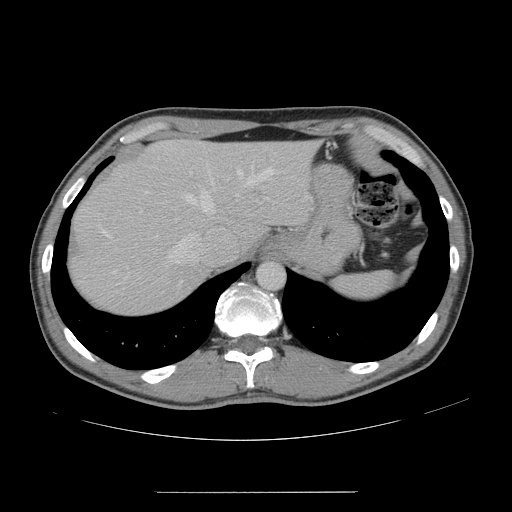
Contrast-enhanced abdominal CT, one axial slice. Position 122 of 178 along the scan axis. 120 kVp. Intravenous contrast given. Soft-tissue window (W 400 / L 40 HU). 512 × 512 image matrix, field of view 401 × 401 mm. Male patient, age 53 years. Case-level facts recorded for this patient, not image findings: diagnosis: colorectal cancer liver metastases, imaged before liver resection; multiple liver metastases: yes; largest metastasis: 2.4 cm; disease in both lobes: no.
Annotated regions visible in this slice (manually delineated by an expert):
- hepatic veins: bounding box (x1, y1, x2, y2) in pixels: (102, 167, 274, 264)
- liver: (69, 140, 318, 315)
- planned liver remnant (the part of the liver to remain after resection): (151, 140, 316, 246)
- portal vein (with intrahepatic branches): (140, 211, 142, 213)